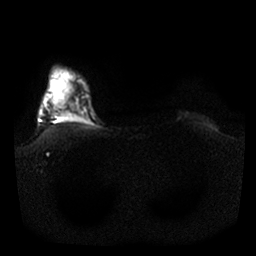
Breast MRI, one axial slice. Position 24 of 25 along the scan axis. Diffusion-weighted series; image 2 of 4 stored at this slice position (different b-values; order by instance number). 1.5 T. 256 × 256 image matrix, field of view 340 × 340 mm. Female patient.
Structures marked on this image (outlined manually by an expert reader):
- tumour on diffusion-weighted imaging: bounding box (x1, y1, x2, y2) in pixels: (52, 79, 79, 111)